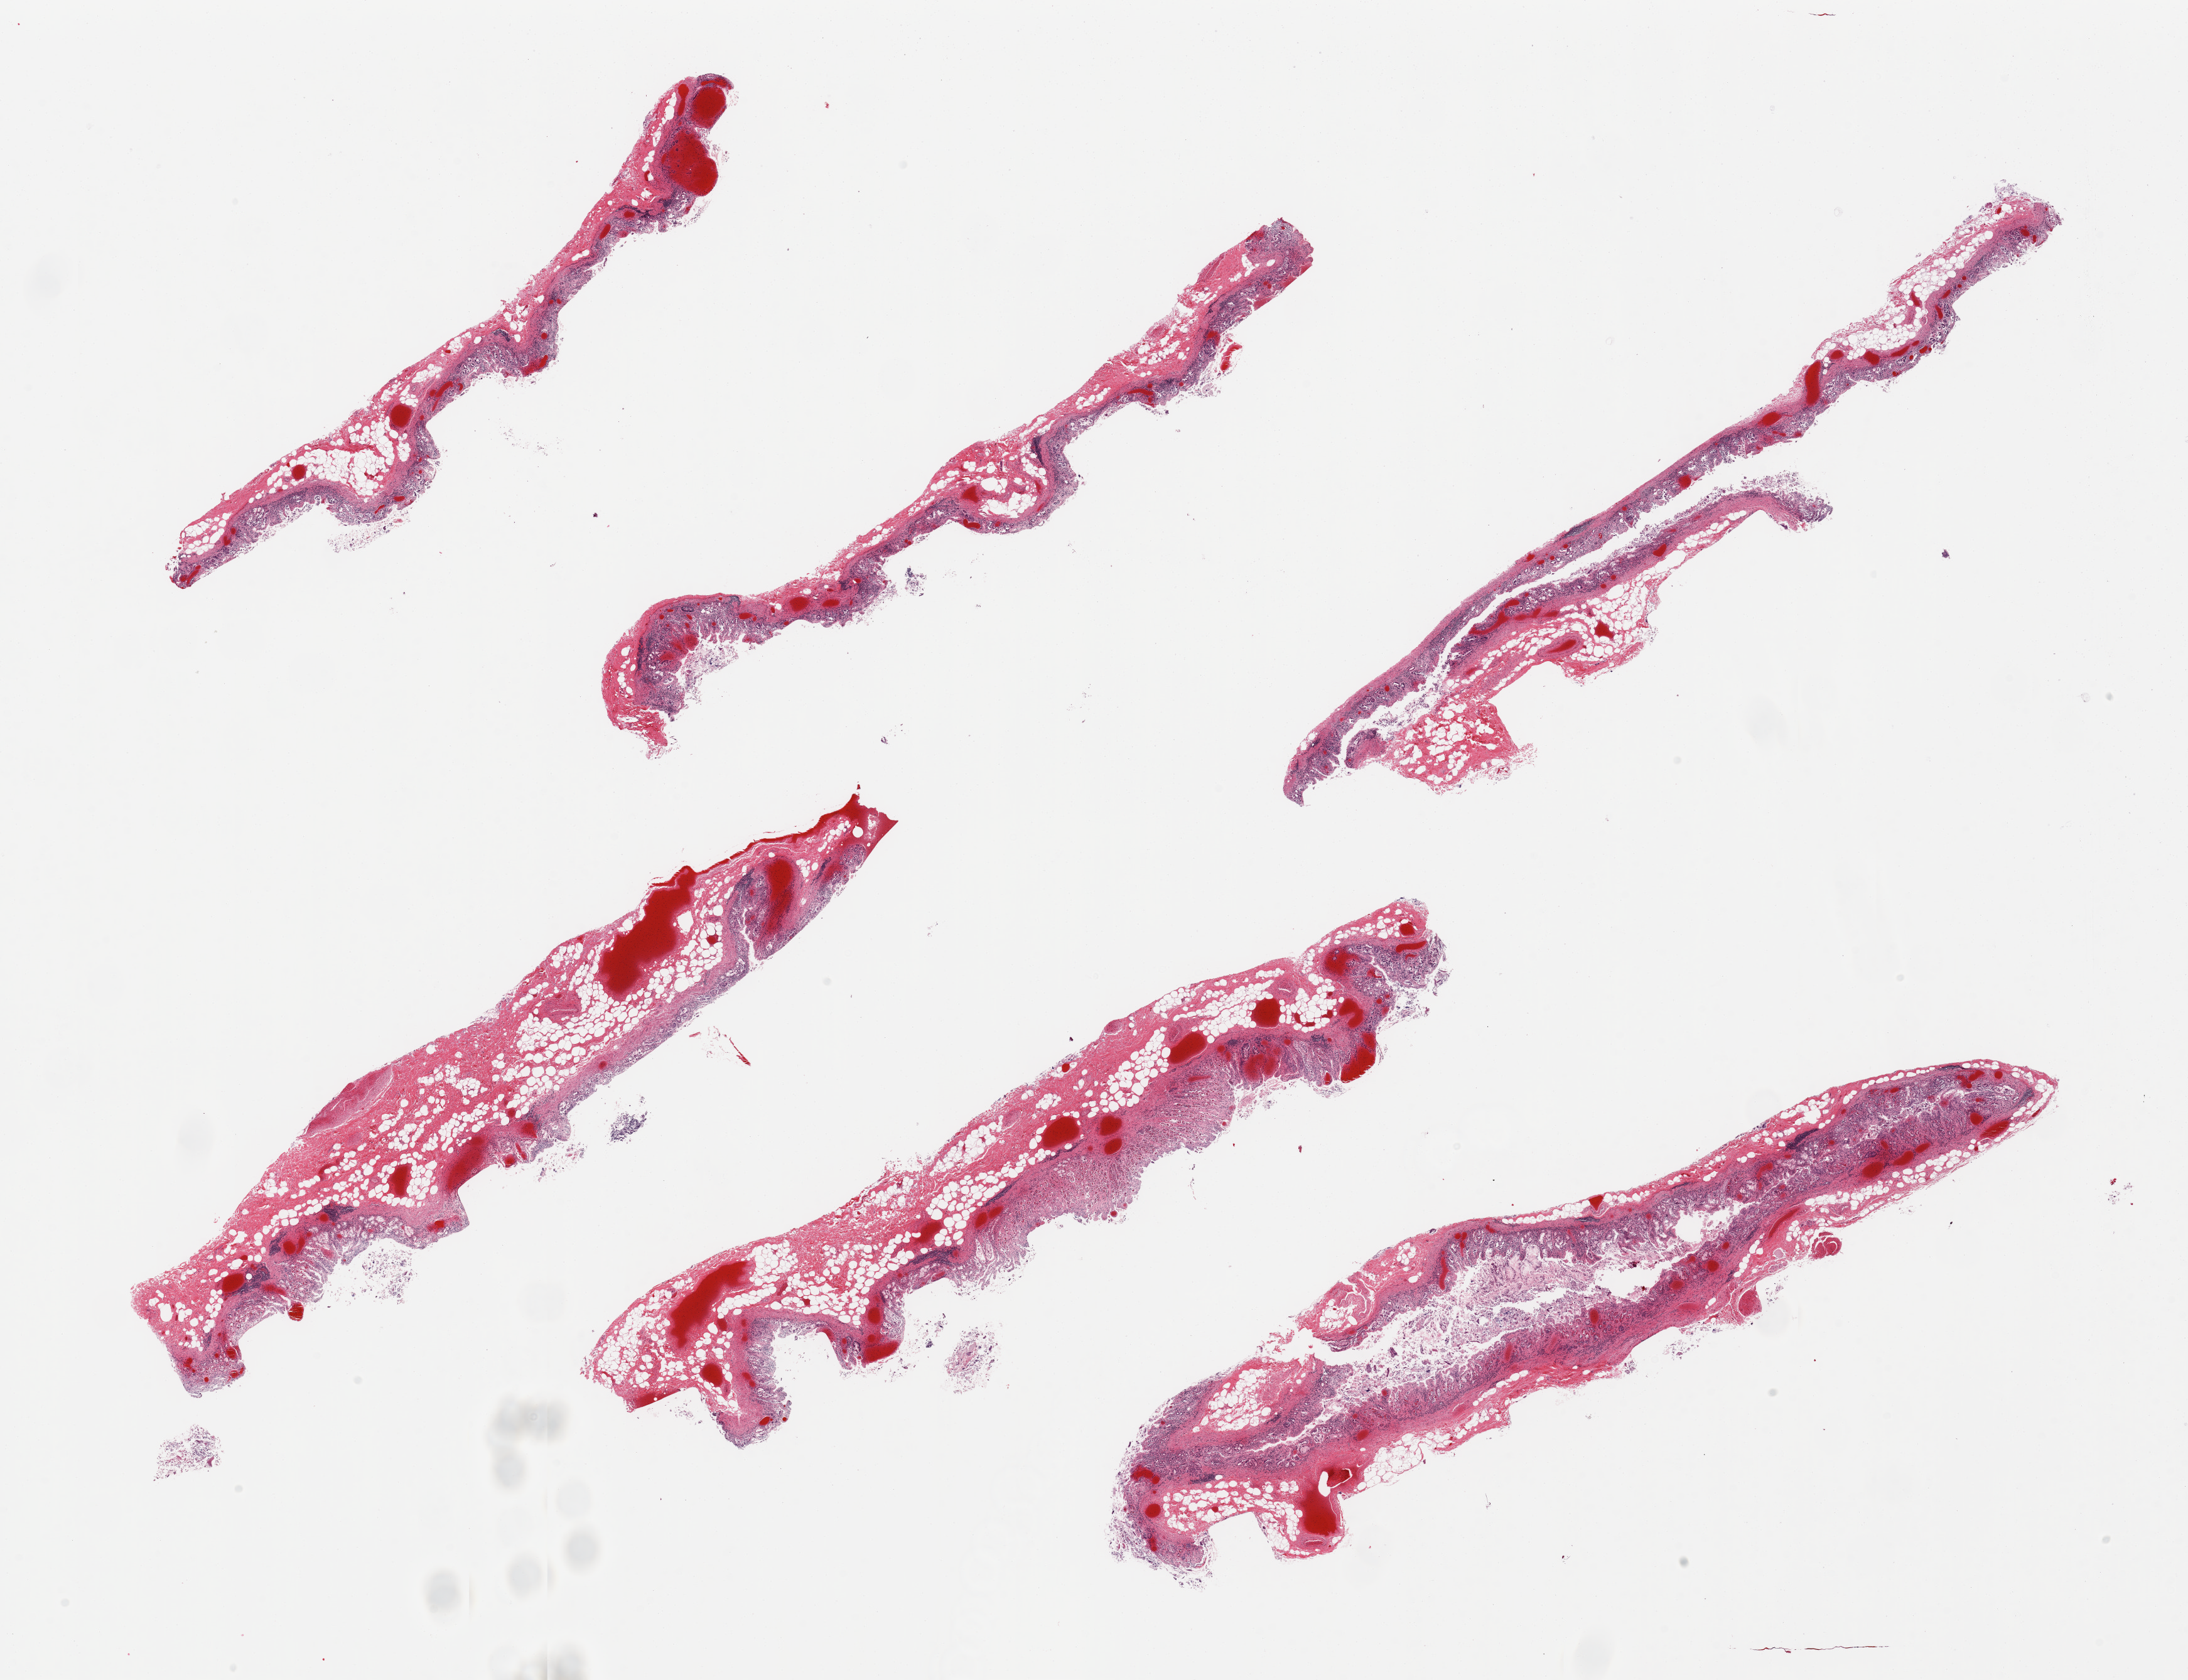
Whole-slide image, hematoxylin and eosin (H&E) stain — whole scanned area (about 27.6 x 21.2 mm) shown as a low-resolution overview, PAXgene-fixed paraffin-embedded (PFPE) section, sampled site (target tissue): stomach, tissue donor sample. Donor sex: male.
* reviewer comment on this tissue sample: 6 pieces; mucosa completely autolyzed, no muscularis propria present